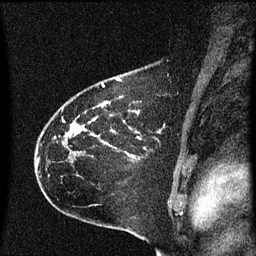
Breast MRI (dynamic contrast-enhanced), one sagittal slice; position 45 of 60 along the scan axis; dynamic contrast-enhanced series, image 2 of 3 at this slice position (ordered by acquisition); 1.5 T; TE 4.2 ms, TR 8.4 ms; 2 mm slice thickness; 256 × 256 image matrix, field of view 200 × 200 mm. Patient: female, 35 years. Case-level facts recorded for this patient, not image findings: setting: breast cancer imaged before/during neoadjuvant chemotherapy; receptor status: HER2-positive.
Outlined on this slice (semi-automatically segmented with operator editing):
- analysis volume of interest (the breast-tissue region the enhancement analysis was run in; not a lesion): bounding box (x1, y1, x2, y2) in pixels: (37, 68, 169, 173)
- tumour enhancement mask (voxels above the 70 % enhancement threshold inside the analysis volume of interest): (65, 104, 104, 143)